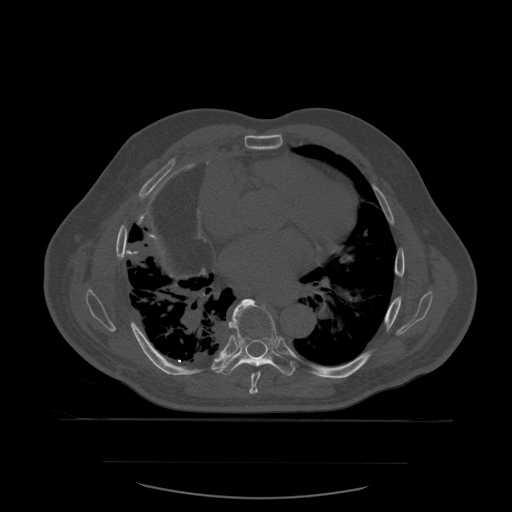
CT including the spine, one axial slice; position 368 of 590 along the scan axis; bone window (W 1800 / L 400 HU); 1.25 mm slice thickness; 512 × 512 image matrix, field of view 479 × 479 mm. Patient age 71 years. From the clinical record (not read from this slice): primary cancer: lung.
Outlined on this slice (semi-automatically segmented with operator editing):
- T7 vertebra: bounding box <249,371,261,395> (left, top, right, bottom; pixels)
- T8 vertebra: <220,299,296,376>